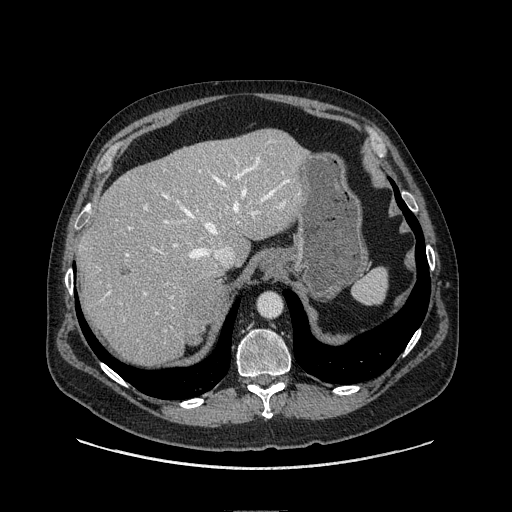
Contrast-enhanced abdominal CT, one axial slice; position 88 of 149 along the scan axis; soft-tissue window (W 400 / L 40 HU); 1.25 mm slice thickness; 512 × 512 image matrix, field of view 440 × 440 mm. Male patient. From the clinical record (not read from this slice): diagnosis: adrenocortical carcinoma; tumour side: right adrenal; tumour size at pathology: 7.5 cm; Ki-67 index: 15 %; stage (as recorded): 2.
Outlined on this slice (semi-automatically segmented with operator editing):
- mass: box from (x=189, y=278) to (x=225, y=346) px